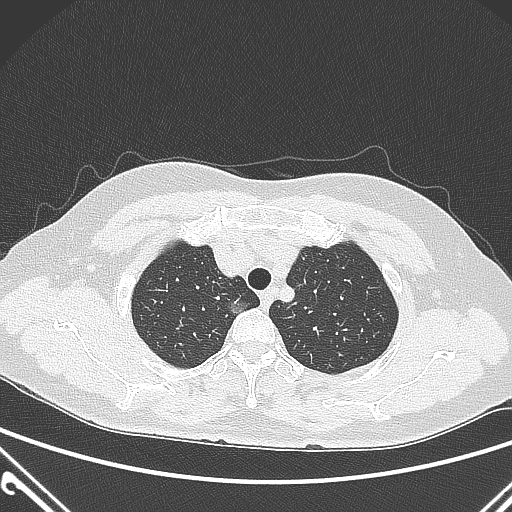
Chest CT, one axial slice. Slice 238 of 300 in the series (ordered by position). 120 kVp. Lung window (W 1500 / L -600 HU). 1 mm slice thickness. 512 × 512 image matrix, field of view 350 × 350 mm. Patient: female, 54 years. From the clinical record (not read from this slice): clinical TNM (as recorded): T1a N0 M0; histopathological grade: G1.
Outlined on this slice (rectangle marked by the reading radiologist):
- lung tumour (recorded histology: adenocarcinoma): bounding box [x1, y1, x2, y2] px = [224, 295, 266, 329]